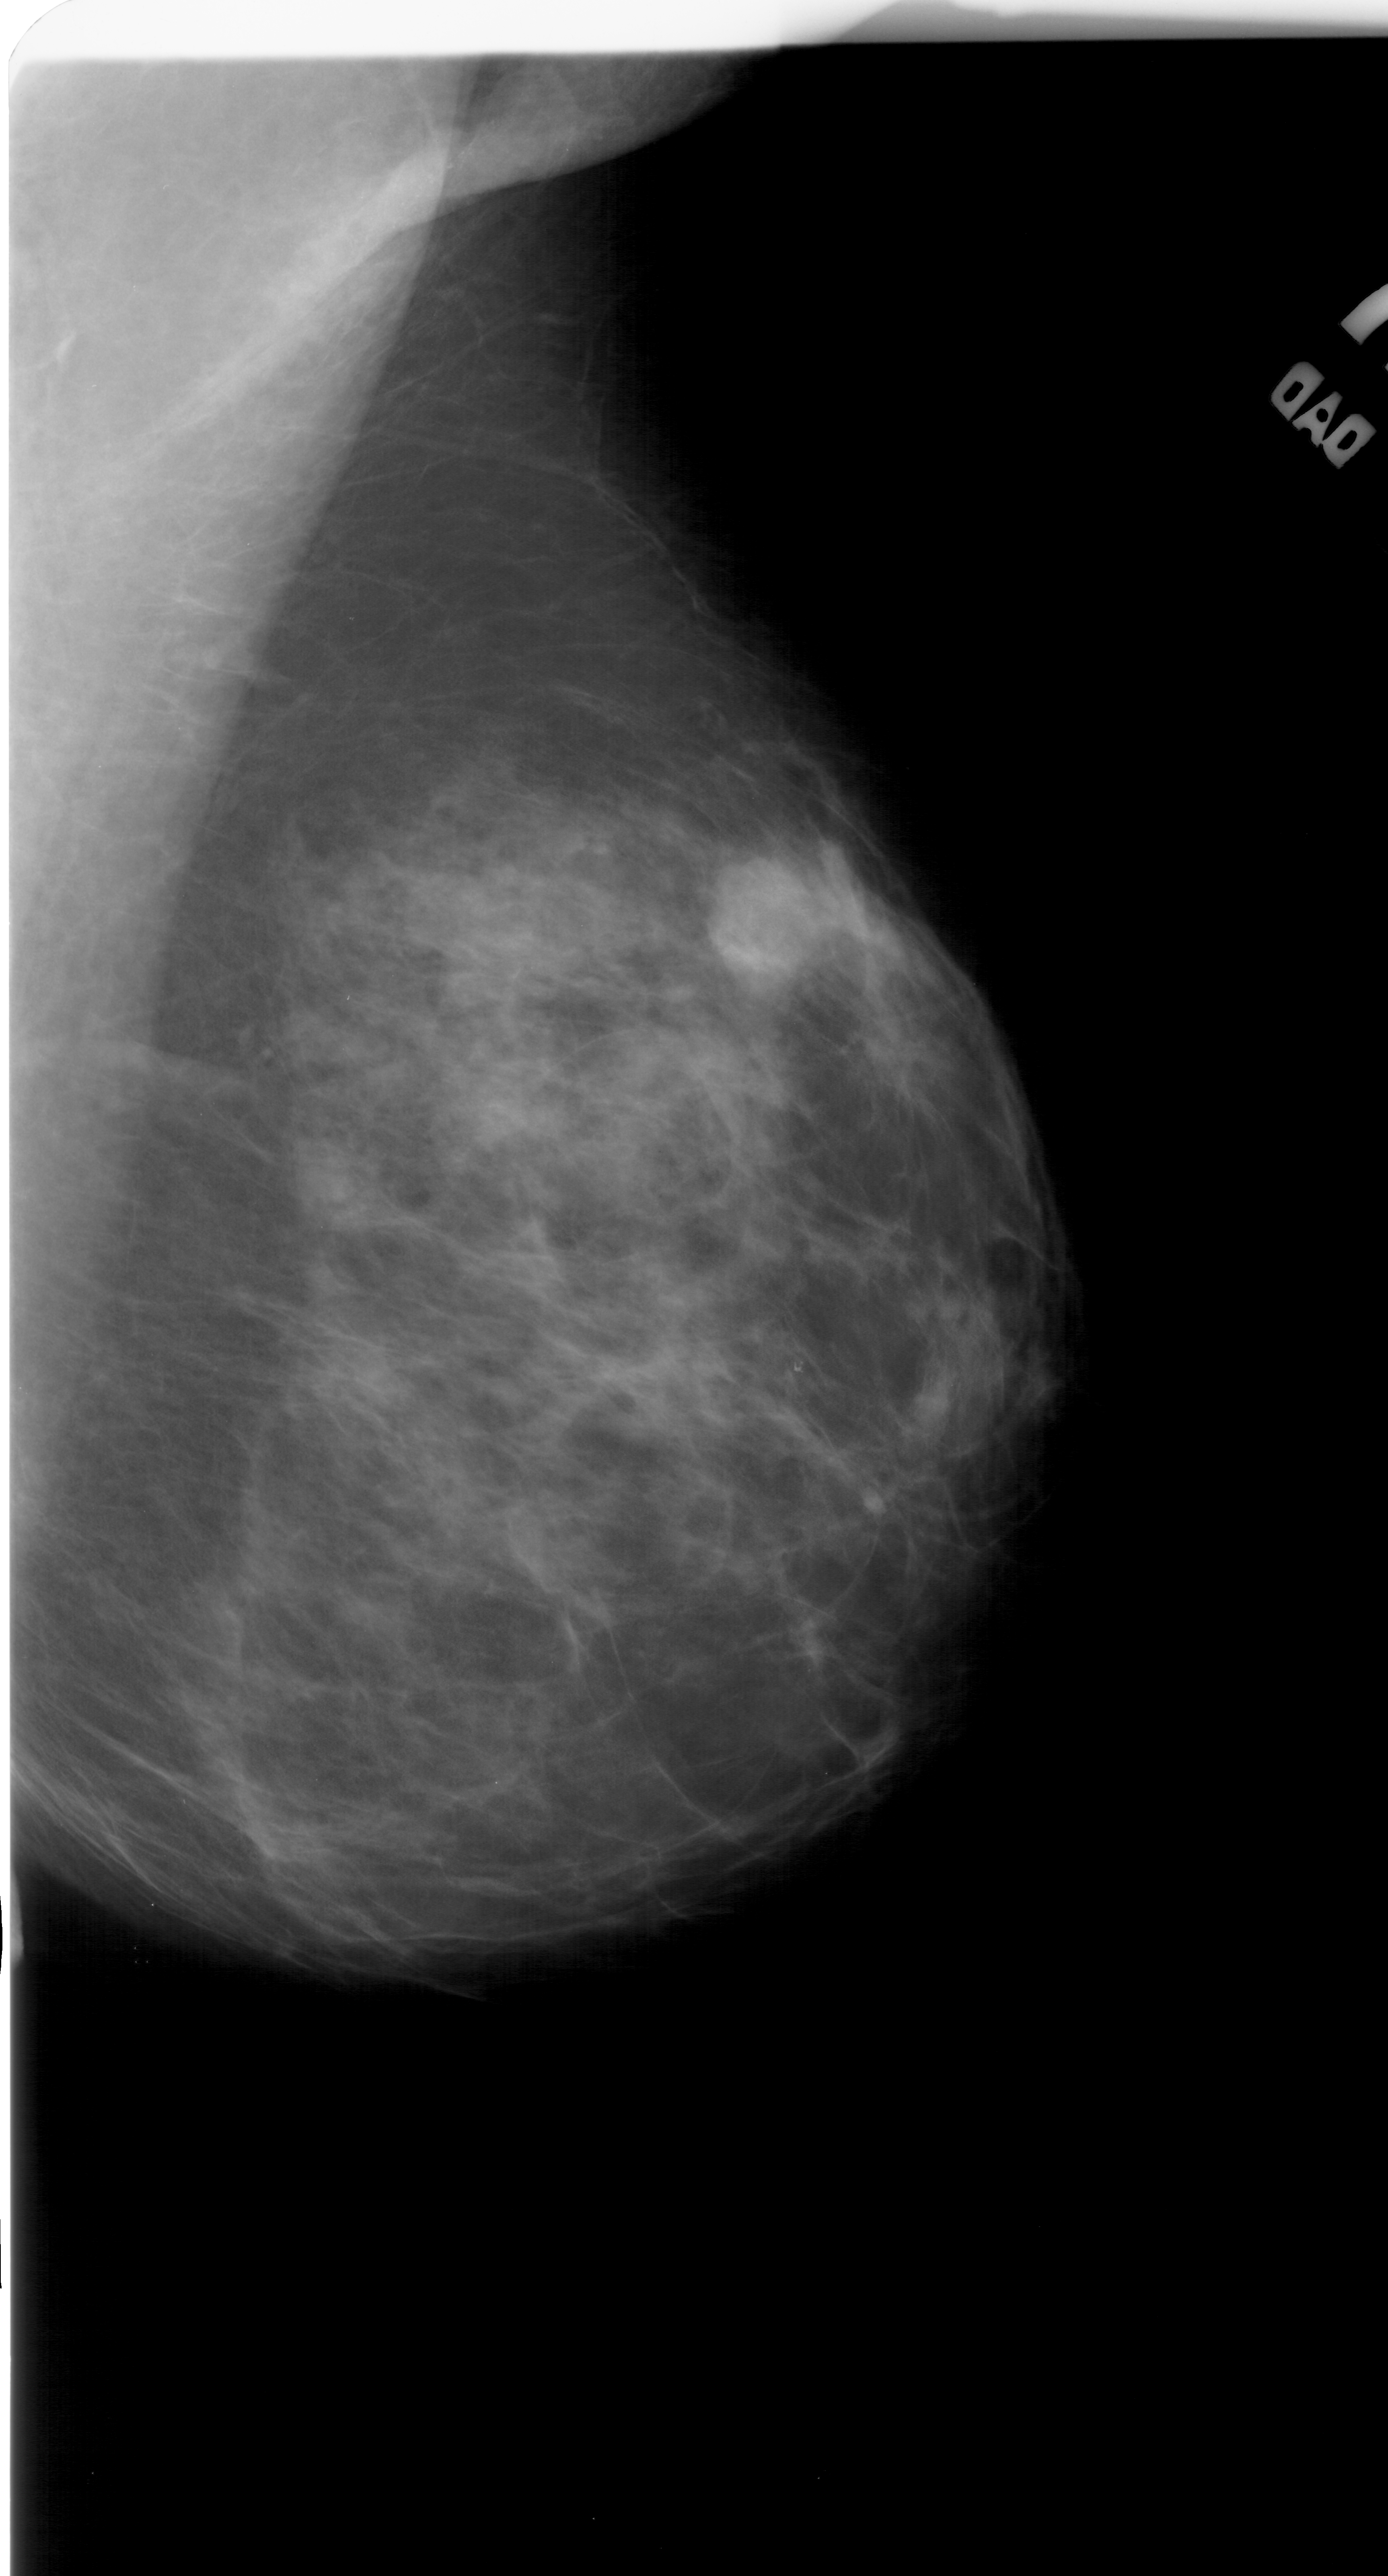
Digitized screen-film mammogram; right breast; MLO view; breast composition: heterogeneously dense (BI-RADS density category 3 of 4); 1388 × 2576 image matrix.
Expert-marked regions of interest on this film, with their recorded descriptors:
- mass, shape lobulated, margins ill defined; BI-RADS assessment category 4; pathology (as recorded): benign: bounding box [x1, y1, x2, y2] px = [704, 860, 809, 984]